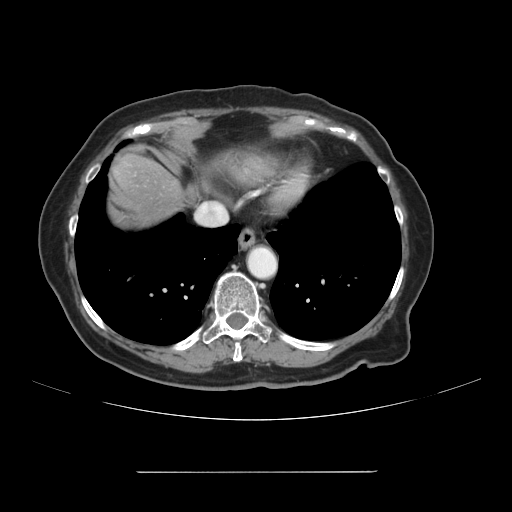
Contrast-enhanced abdominal CT, one axial slice; position 102 of 111 along the scan axis; 120 kVp; soft-tissue window (W 400 / L 40 HU); 2.5 mm slice thickness; 512 × 512 image matrix, field of view 400 × 400 mm. Female patient, age 74 years. From the clinical record (not read from this slice): diagnosis: colorectal cancer liver metastases, imaged before liver resection; multiple liver metastases: yes; largest metastasis: 1.1 cm; chemotherapy before resection: yes.
Annotated regions visible in this slice (outlined manually by an expert reader):
- liver: bounding box [x1, y1, x2, y2] px = [107, 152, 237, 226]